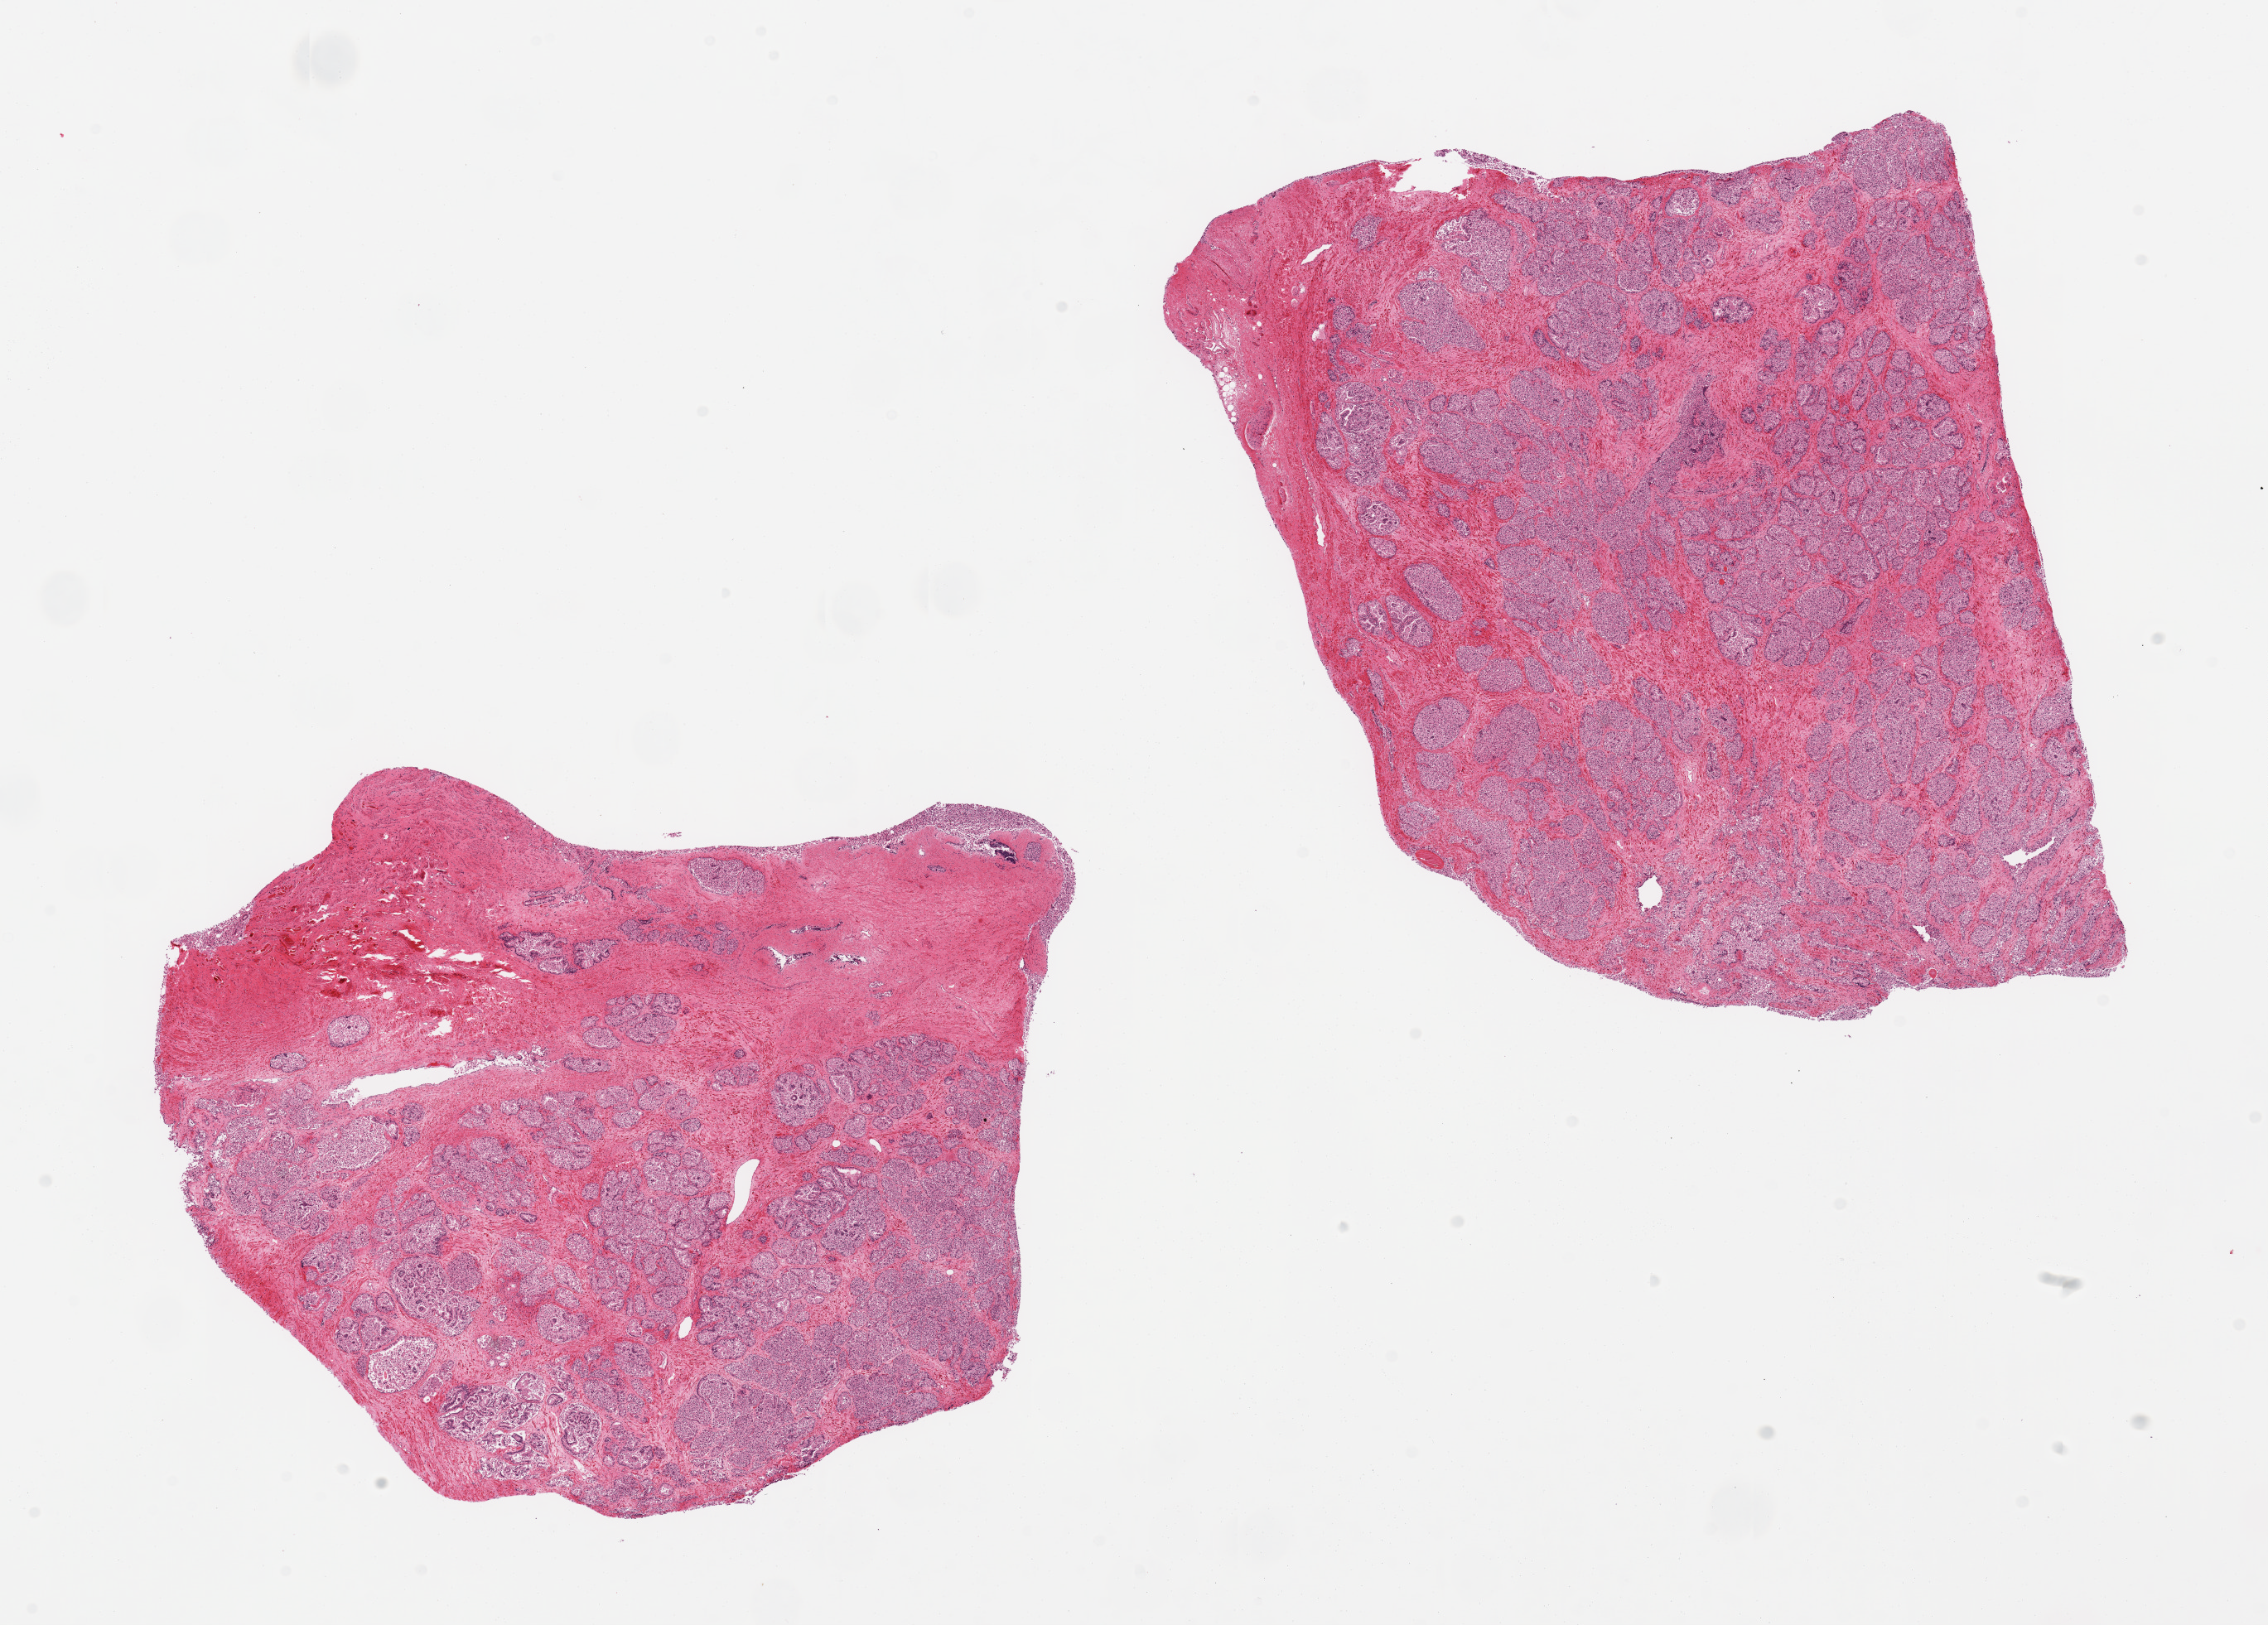
Digitized haematoxylin and eosin-stained section, brightfield — a low-resolution overview of the entire scanned area, about 21.7 x 15.5 mm (slide scanned at 20x); PAXgene-fixed paraffin-embedded (PFPE) section; sampled site (target tissue): prostate; donor tissue sample.
• review note (as recorded): 2 pieces, epithelium sloughed